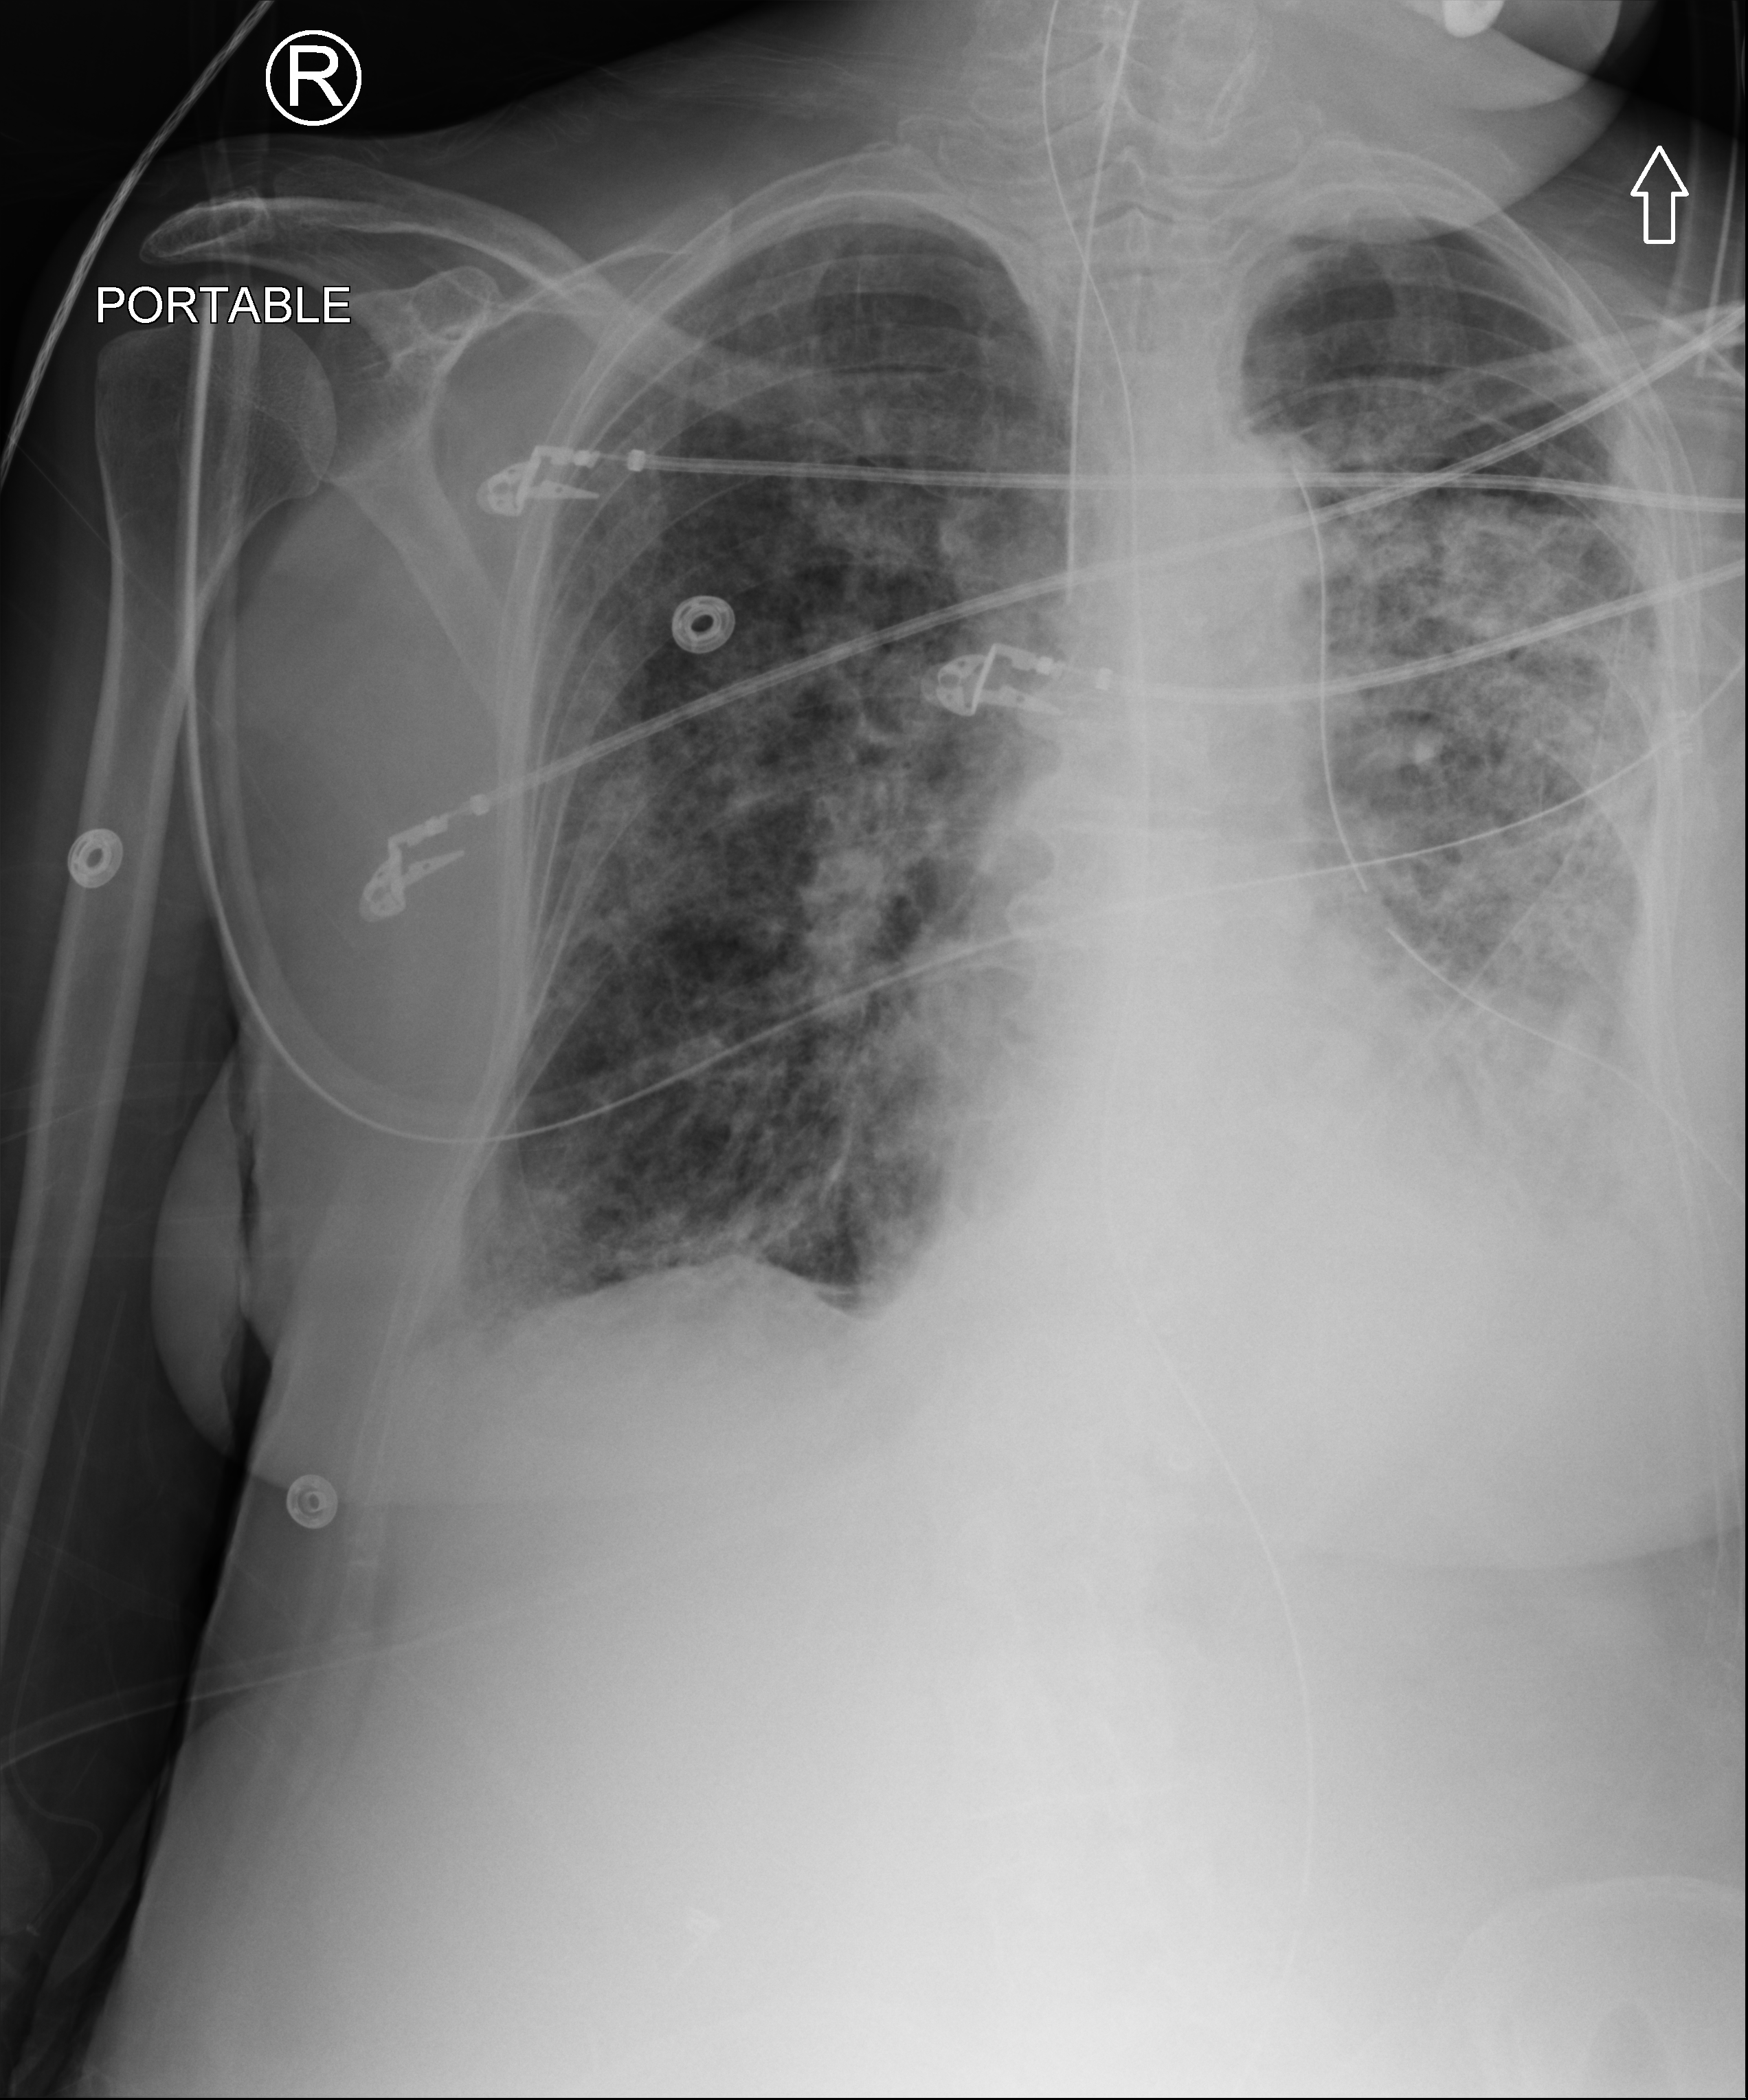
Bedside chest radiograph (computed radiography). Female patient hospitalised with COVID-19, age 75–90 years.
From the hospital-stay record, not from the radiograph (when in the stay this image was taken is not recorded):
- COPD (admission record): no
- mechanically ventilated during this hospital stay: yes